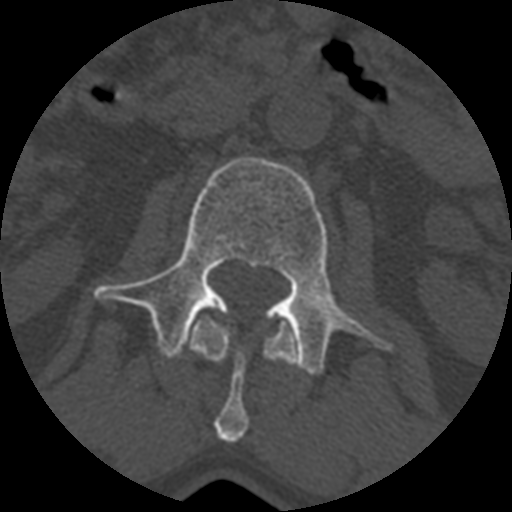
CT including the spine, one axial slice. Position 340 of 399 along the scan axis. Bone window (W 1800 / L 400 HU). 512 × 512 image matrix, field of view 160 × 160 mm. Patient age 71 years. From the clinical record (not read from this slice): primary cancer: prostate.
Structures marked on this image (semi-automatically segmented with operator editing):
- L1 vertebra: box from (x=189, y=310) to (x=296, y=442) px
- L2 vertebra: (x=94, y=157)–(x=394, y=377)